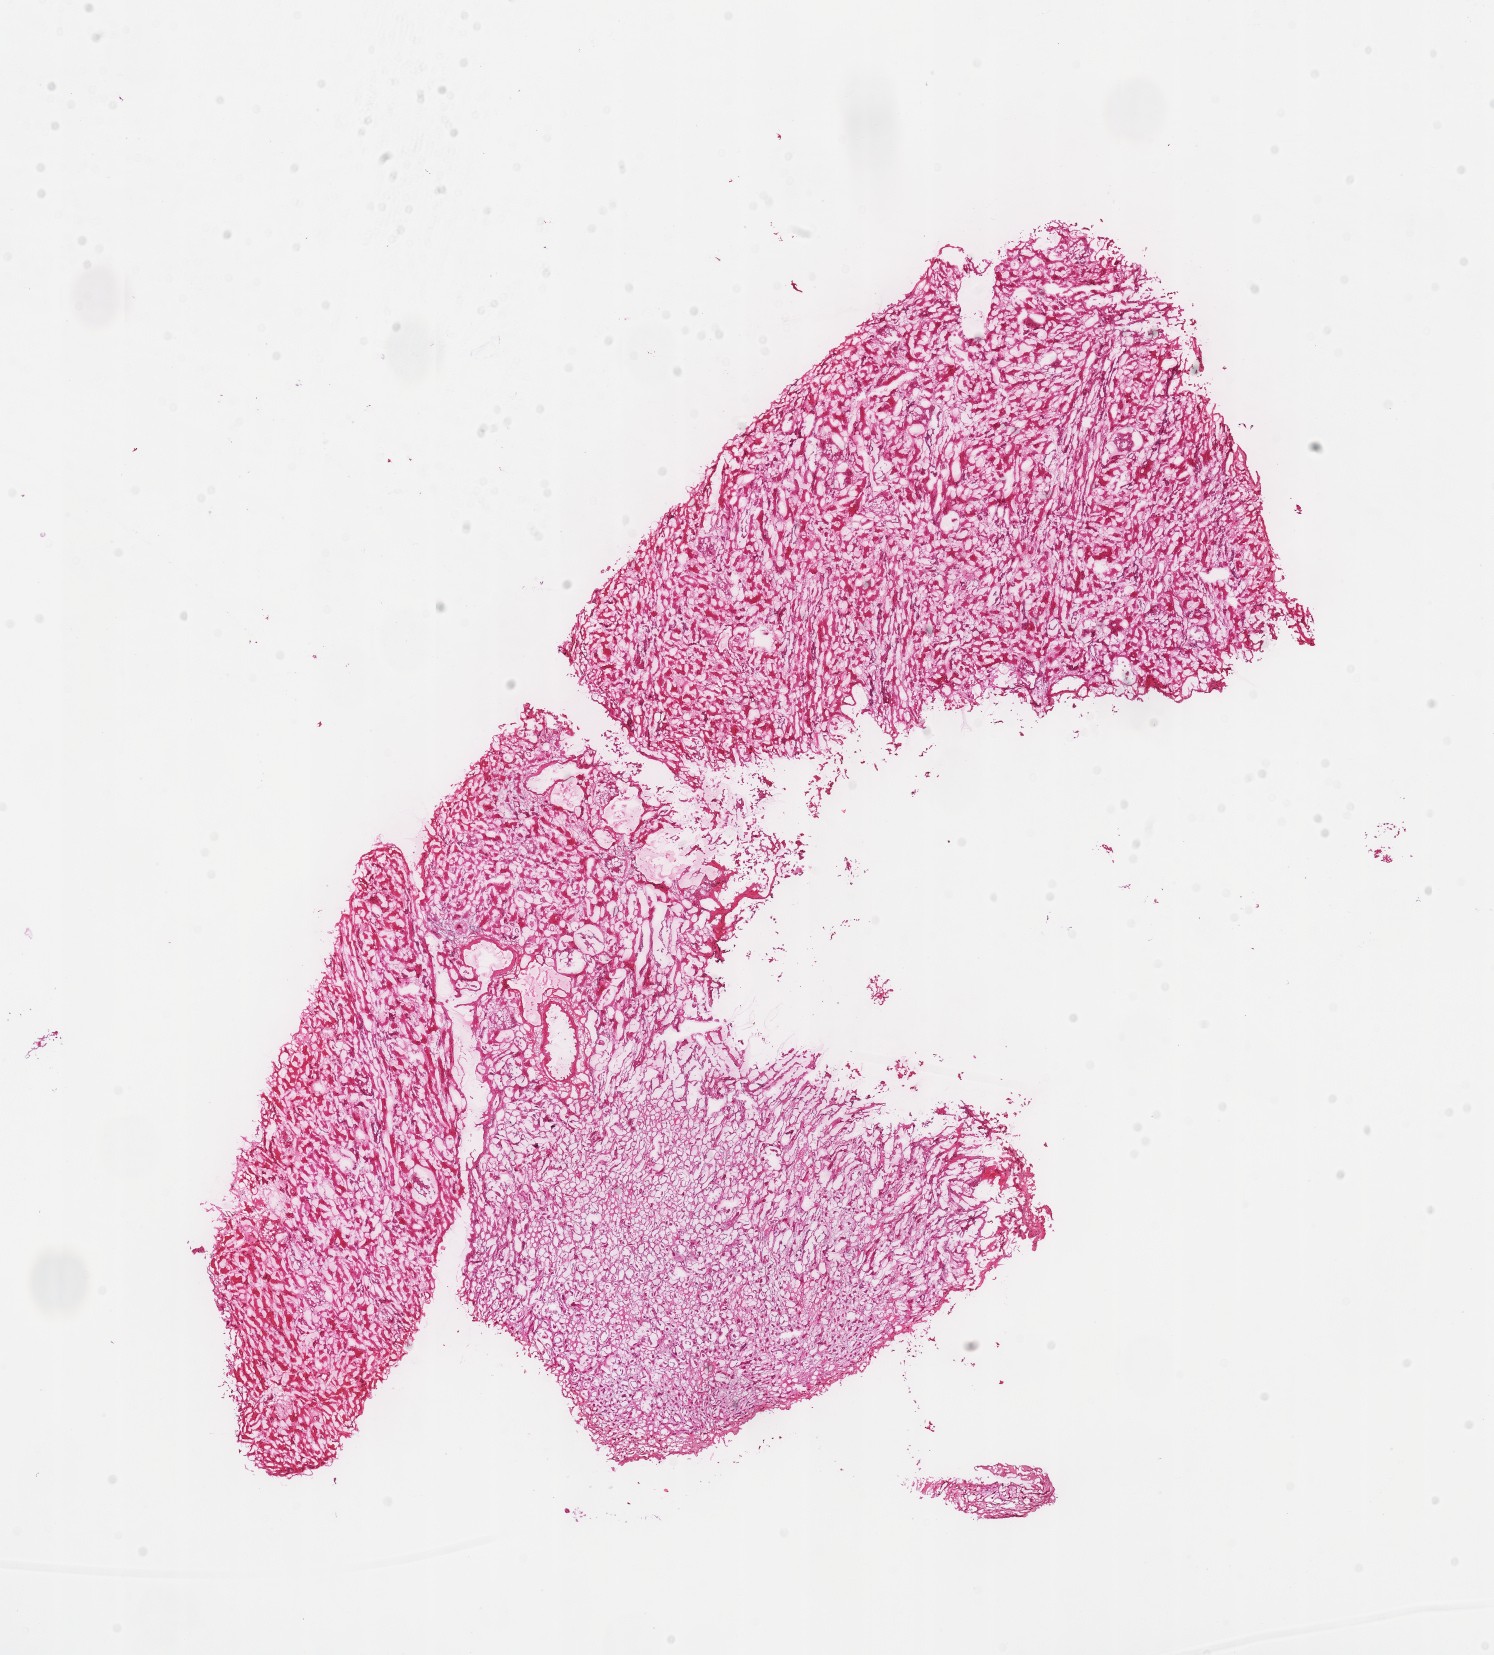
Digitized H&E-stained tissue section (whole slide), whole scanned area (about 11.7 x 13.0 mm, slide scanned at 40x) shown as a low-resolution overview; frozen section; sample: solid tissue normal (non-tumour tissue), kidney. Patient: male, age at initial diagnosis 46 years.
• this section: solid tissue normal (non-tumour) sample from the same patient
• patient diagnosis: Renal cell carcinoma, chromophobe type